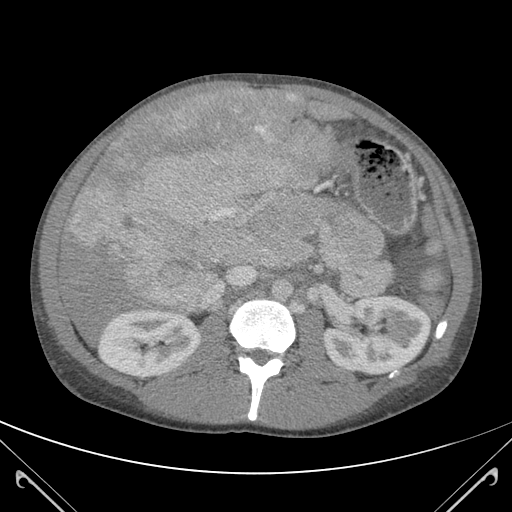
Contrast-enhanced abdominal CT (liver protocol), one axial slice; slice 60 of 118 in the series (ordered by position); 120 kVp; soft-tissue window (W 400 / L 40 HU); 3 mm slice thickness; 512 × 512 image matrix, field of view 380 × 380 mm. From the clinical record (not read from this slice): diagnosis: hepatocellular carcinoma (patient treated with transarterial chemoembolisation; whether this scan precedes or follows treatment is not stated here); TNM stage (as recorded): Stage-IIIB; Child-Pugh class: A; tumour nodularity: uninodular.
Outlined on this slice (semi-automatic segmentation, software-assisted and operator-edited):
- abdominal aorta: bounding box [x1, y1, x2, y2] px = [272, 279, 290, 299]
- liver parenchyma outside the tumour (the mass and vessels are separate outlines, so this box may not span the whole liver): [58, 88, 343, 342]
- mass: [70, 90, 331, 318]
- liver vessels: [204, 236, 268, 302]